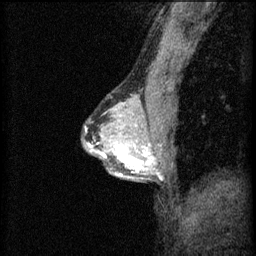
Breast MRI (dynamic contrast-enhanced), one sagittal slice. Slice 38 of 60 in the series (ordered by position). 3 images stored at this slice position (order not interpretable as contrast timing). 1.5 T. TE 4.2 ms, TR 8.2 ms. 2 mm slice thickness. 256 × 256 image matrix. Female patient, age 44 years.
Annotated regions visible in this slice (semi-automatic segmentation, software-assisted and operator-edited):
- analysis volume of interest (the breast-tissue region the enhancement analysis was run in; not a lesion): box from (x=102, y=132) to (x=151, y=181) px
- tumour enhancement mask (voxels above the 70 % enhancement threshold inside the analysis volume of interest): (x=102, y=140)–(x=151, y=179)